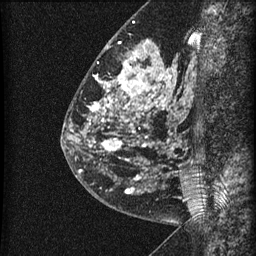
Breast MRI (dynamic contrast-enhanced), one sagittal slice; position 23 of 60 along the scan axis; dynamic contrast-enhanced series, image 2 of 3 at this slice position (ordered by acquisition); 1.5 T; TE 4.2 ms, TR 22.7 ms; 1.5 mm slice thickness; 256 × 256 image matrix, field of view 180 × 180 mm. Female patient, age 48 years. From the clinical record (not read from this slice): setting: breast cancer imaged before/during neoadjuvant chemotherapy; receptor status: triple-negative.
Outlined on this slice (semi-automatically segmented with operator editing):
- analysis volume of interest (the breast-tissue region the enhancement analysis was run in; not a lesion): bounding box <81,23,186,202> (left, top, right, bottom; pixels)
- tumour enhancement mask (voxels above the 90 % enhancement threshold inside the analysis volume of interest): <90,42,174,191>